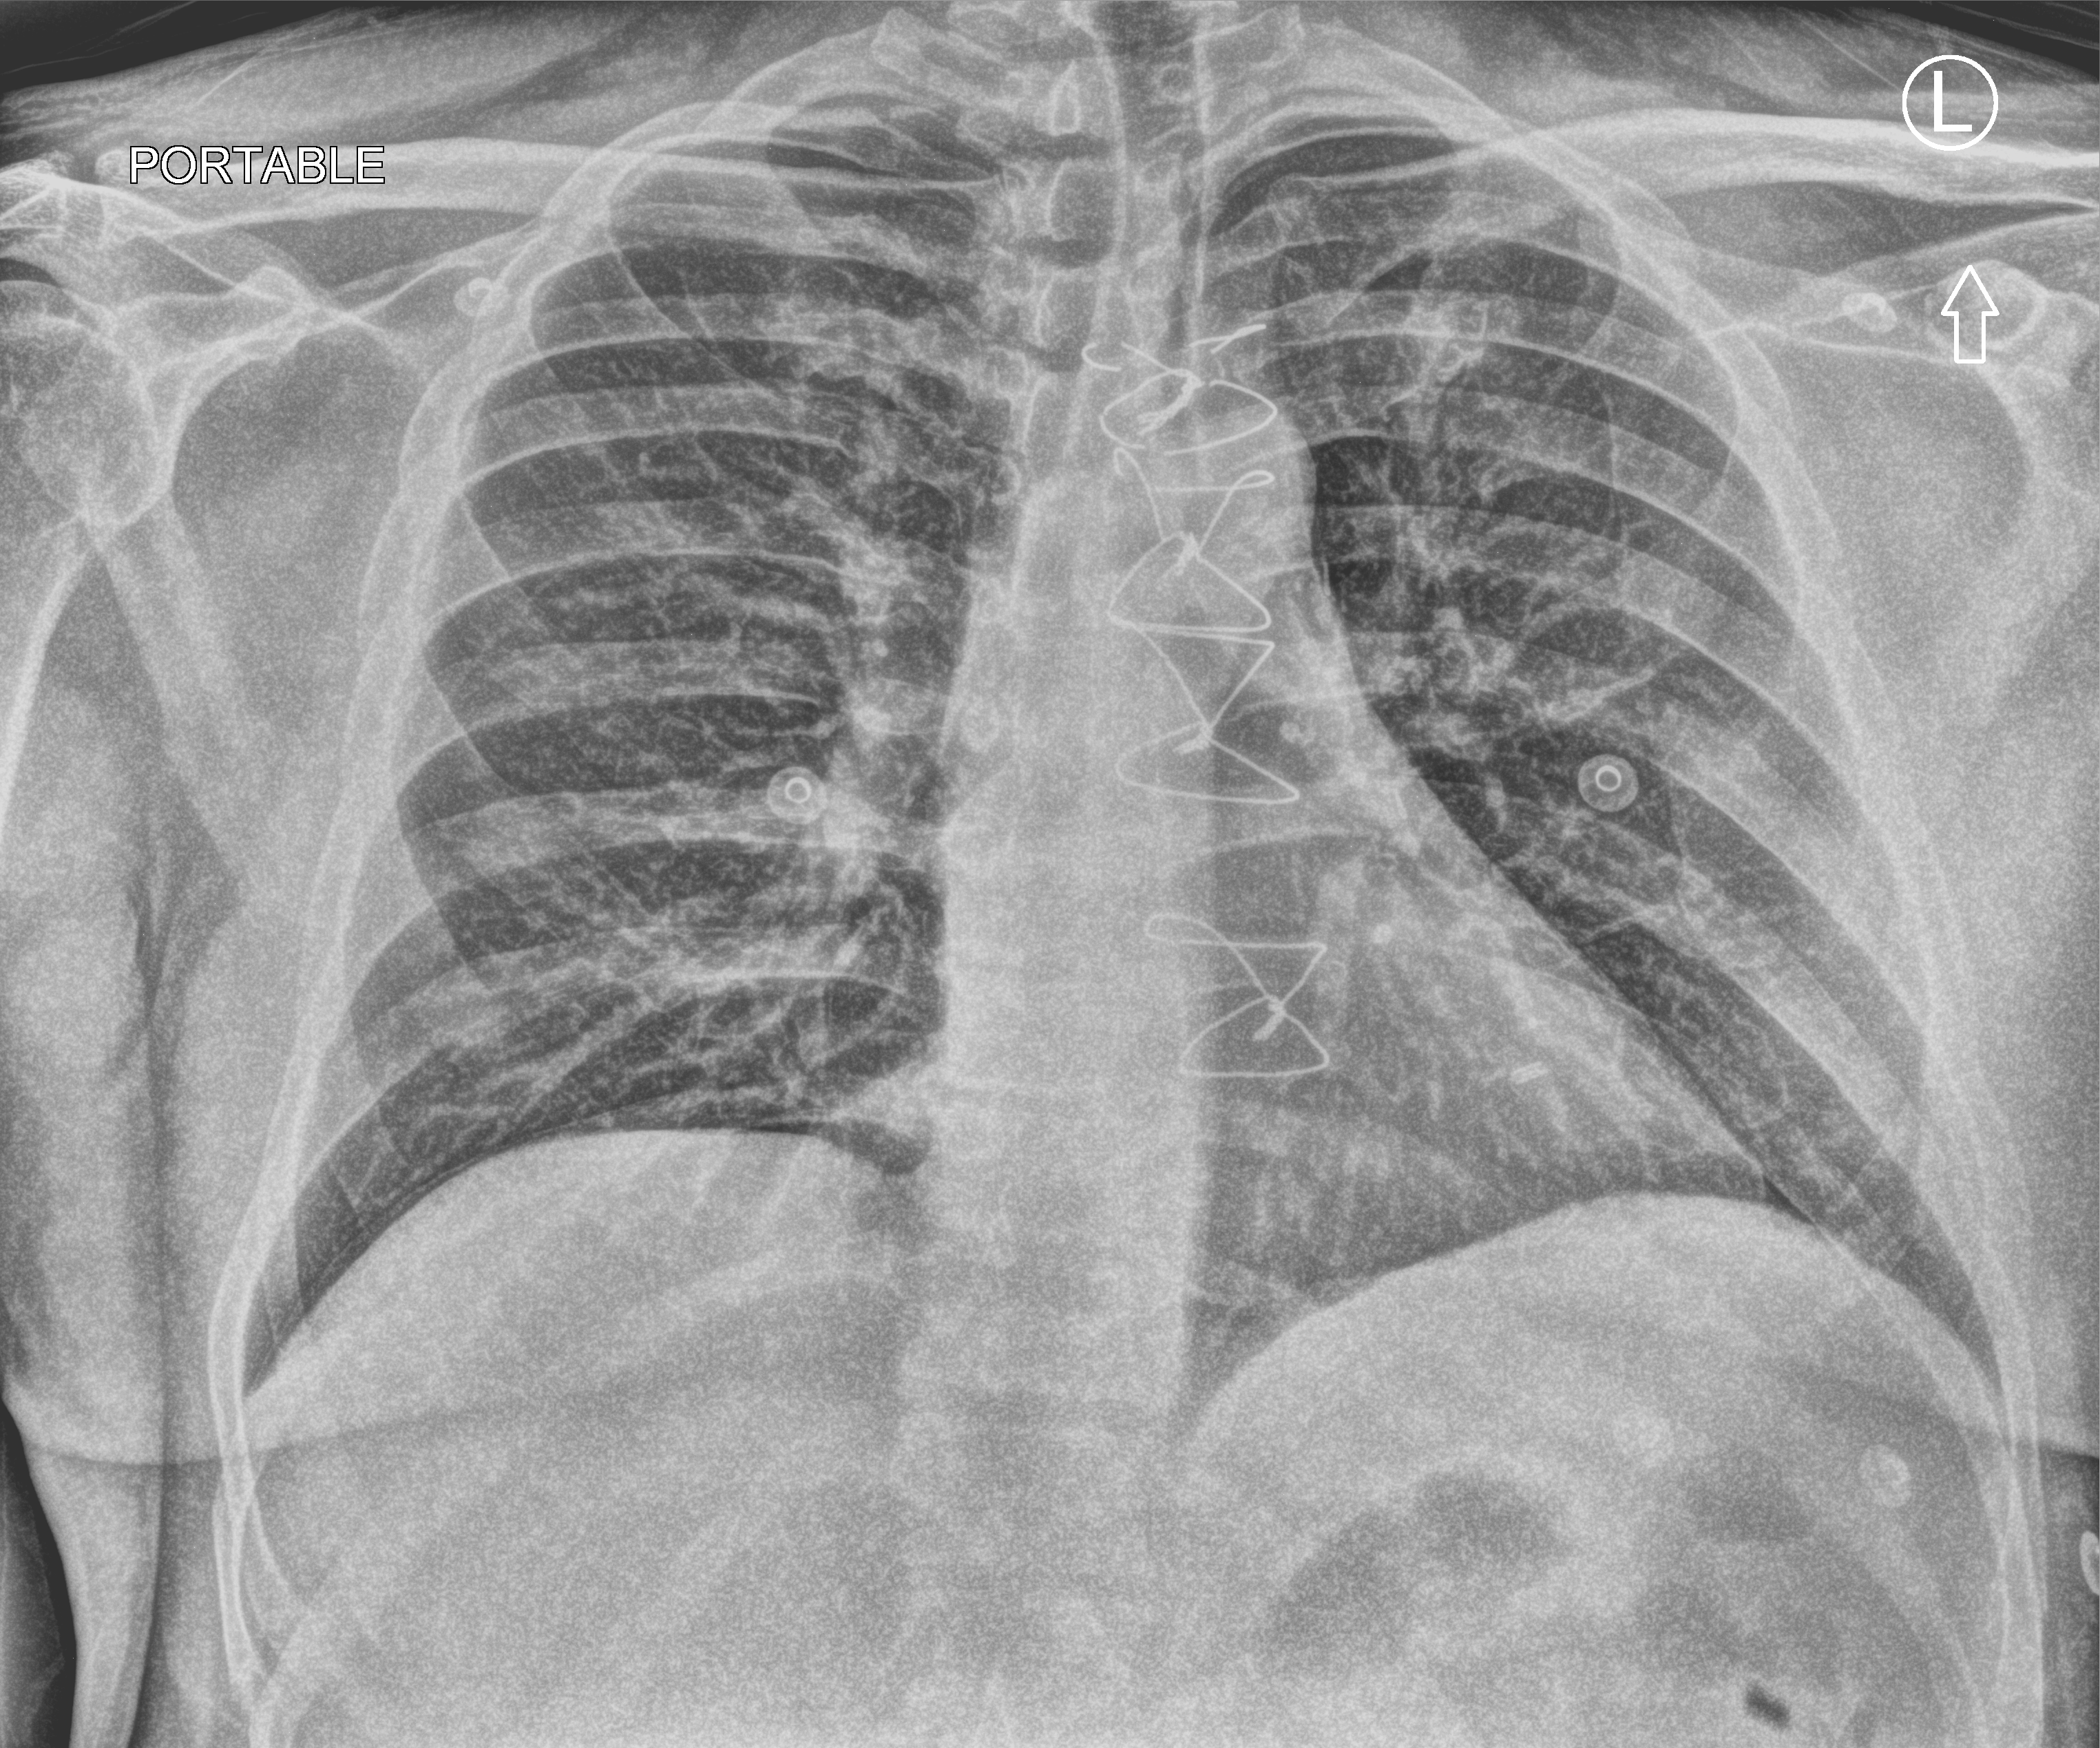
Chest X-ray (portable), anteroposterior (AP) projection. Patient hospitalised with COVID-19; male, aged 18–59 years.
Hospital-stay facts (about this admission, not read from this image; timing relative to this image not recorded):
- hypertension (admission record): yes
- diabetes (admission record): no
- mechanically ventilated during this hospital stay: no